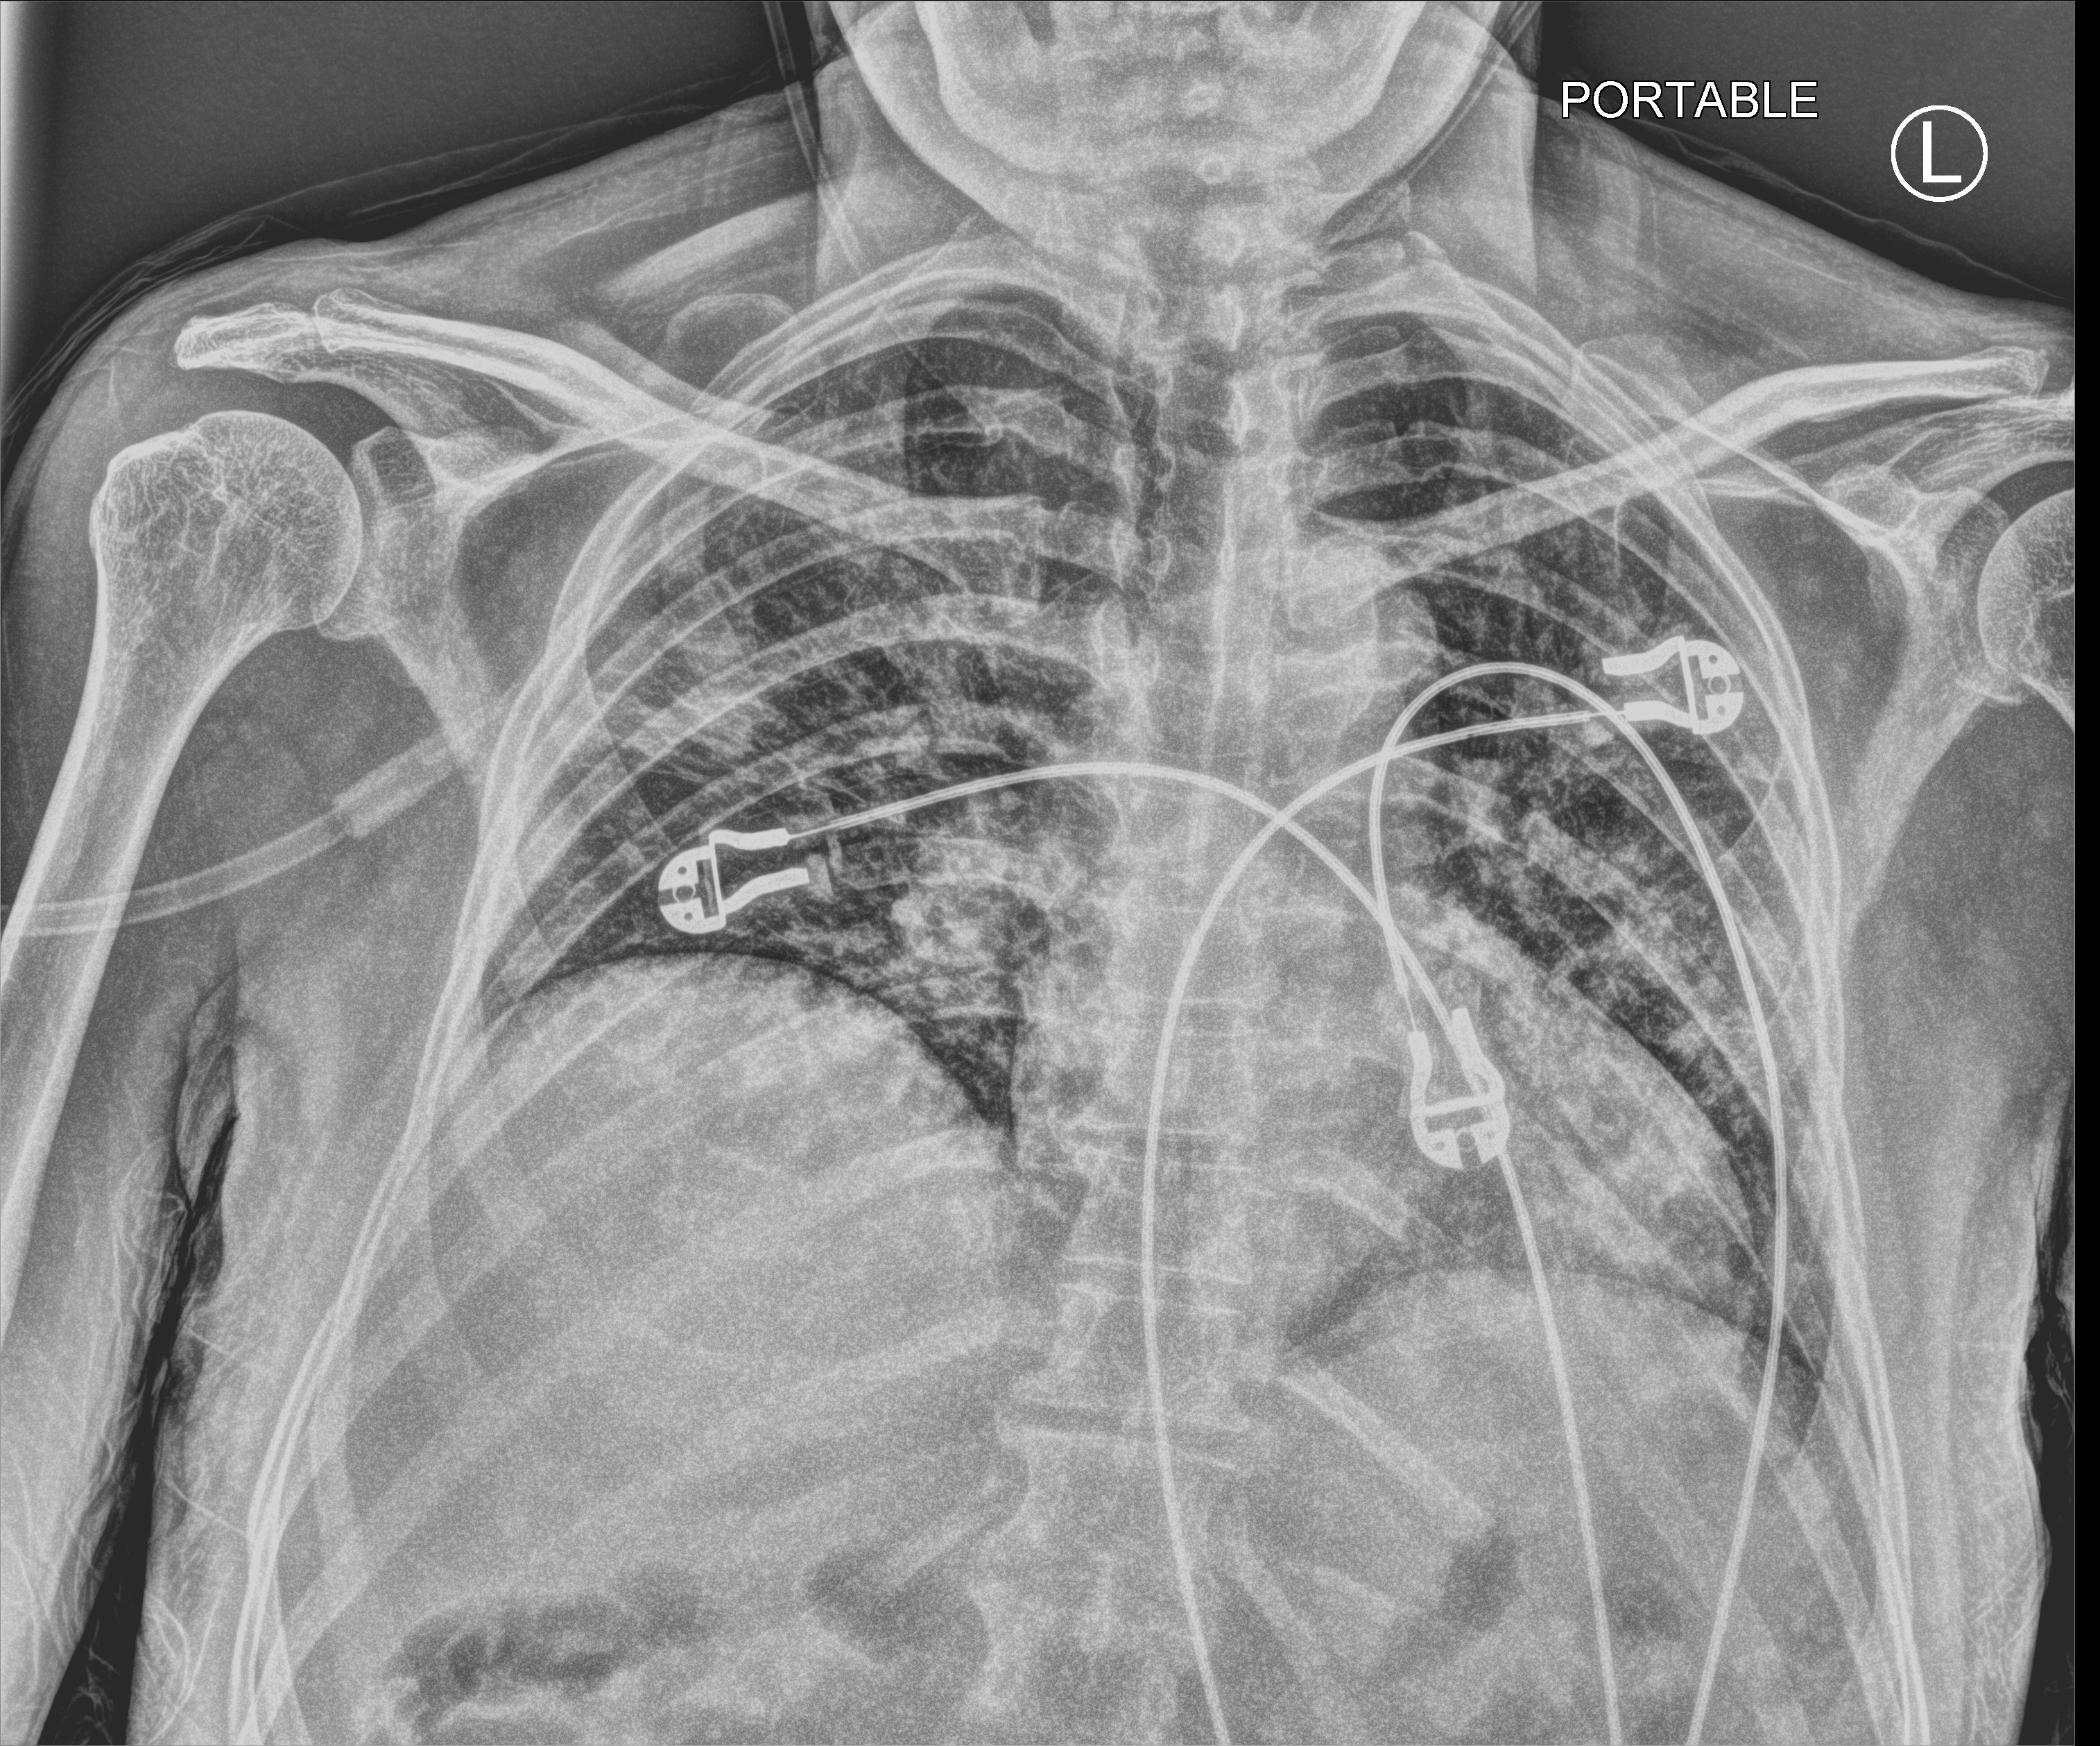
Chest X-ray (portable); anteroposterior (AP) projection. Male patient hospitalised with COVID-19, age 60–74 years.
From the hospital-stay record, not from the radiograph (when in the stay this image was taken is not recorded): admitted to intensive care during this hospital stay: no.